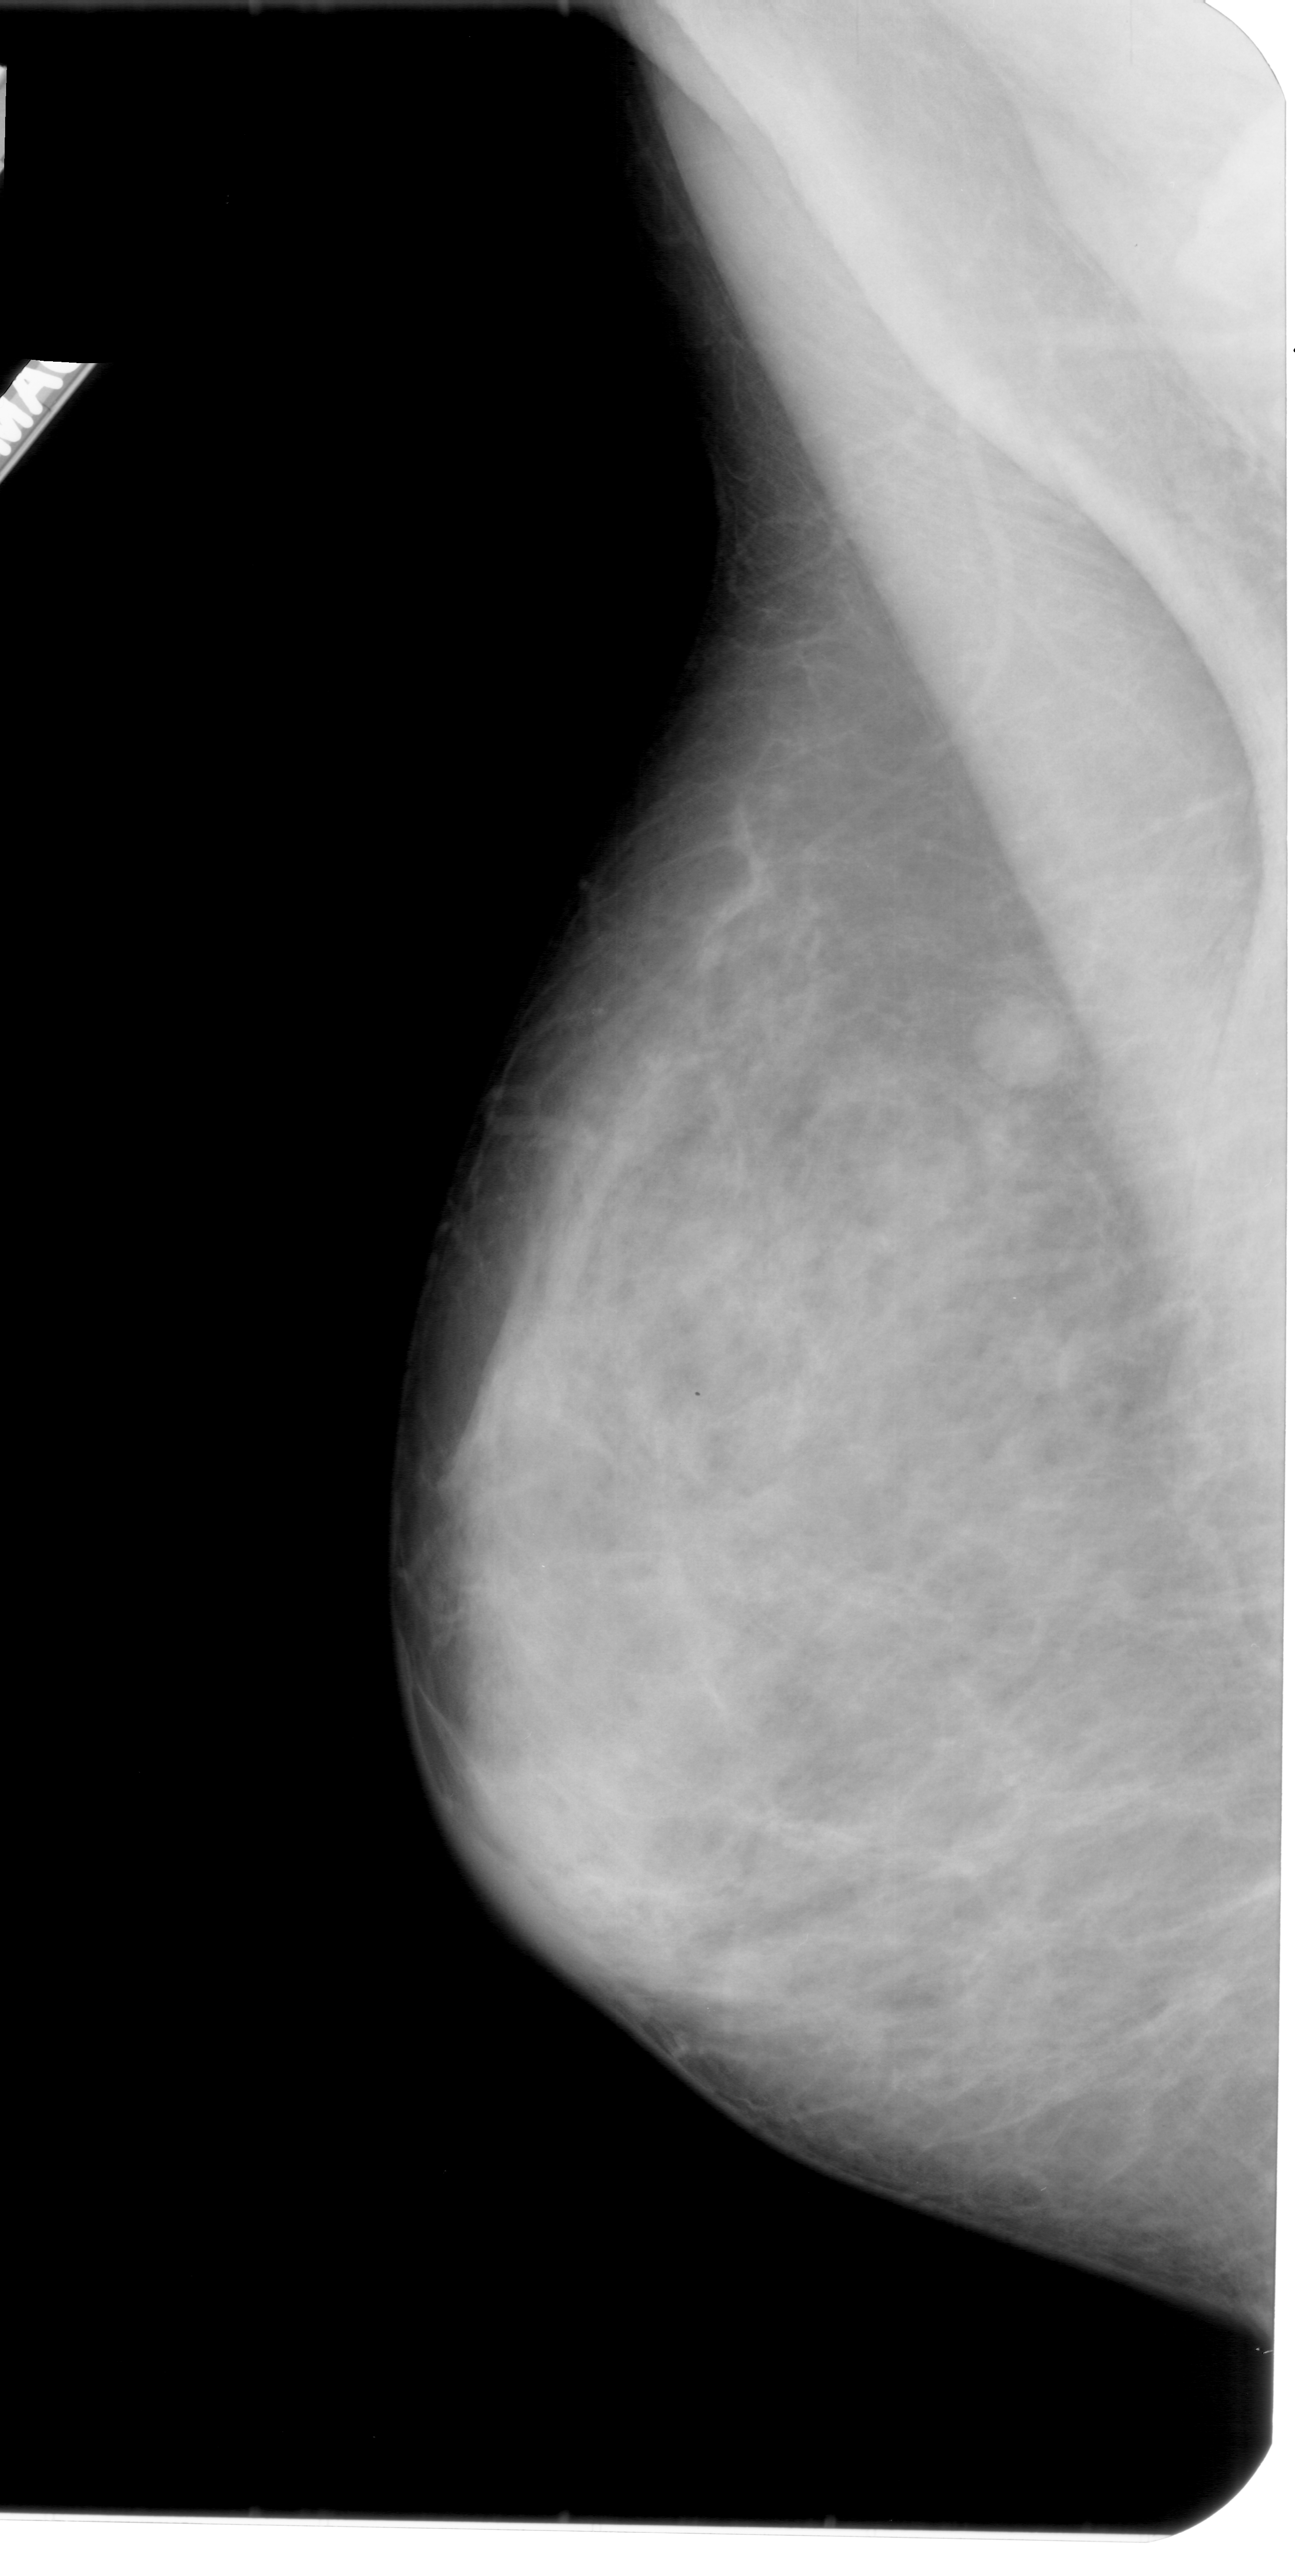
Mammogram (digitized film); left breast; mediolateral oblique (MLO) view; BI-RADS breast density category 3 (scale 1–4).
Abnormality record for this image: mass, shape round, margins circumscribed; BI-RADS assessment category 3; subtlety rating 4 on a 1 (subtle) to 5 (obvious) scale; pathology (as recorded): benign.